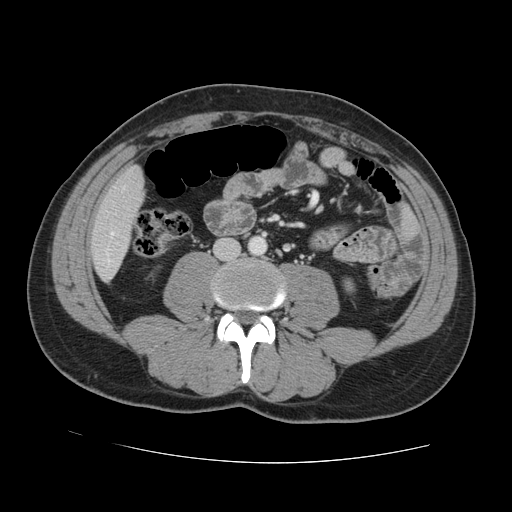
Contrast-enhanced abdominal CT, one axial slice; position 22 of 131 along the scan axis; 120 kVp; soft-tissue window (W 400 / L 40 HU); 2.5 mm slice thickness; 512 × 512 image matrix. Male patient, age 40 years. From the clinical record (not read from this slice): diagnosis: colorectal cancer liver metastases, imaged before liver resection; multiple liver metastases: yes; largest metastasis: 2.9 cm; chemotherapy before resection: yes.
Outlined on this slice (outlined manually by an expert reader):
- hepatic veins: bounding box <111,232,113,236> (left, top, right, bottom; pixels)
- liver: <92,168,143,279>